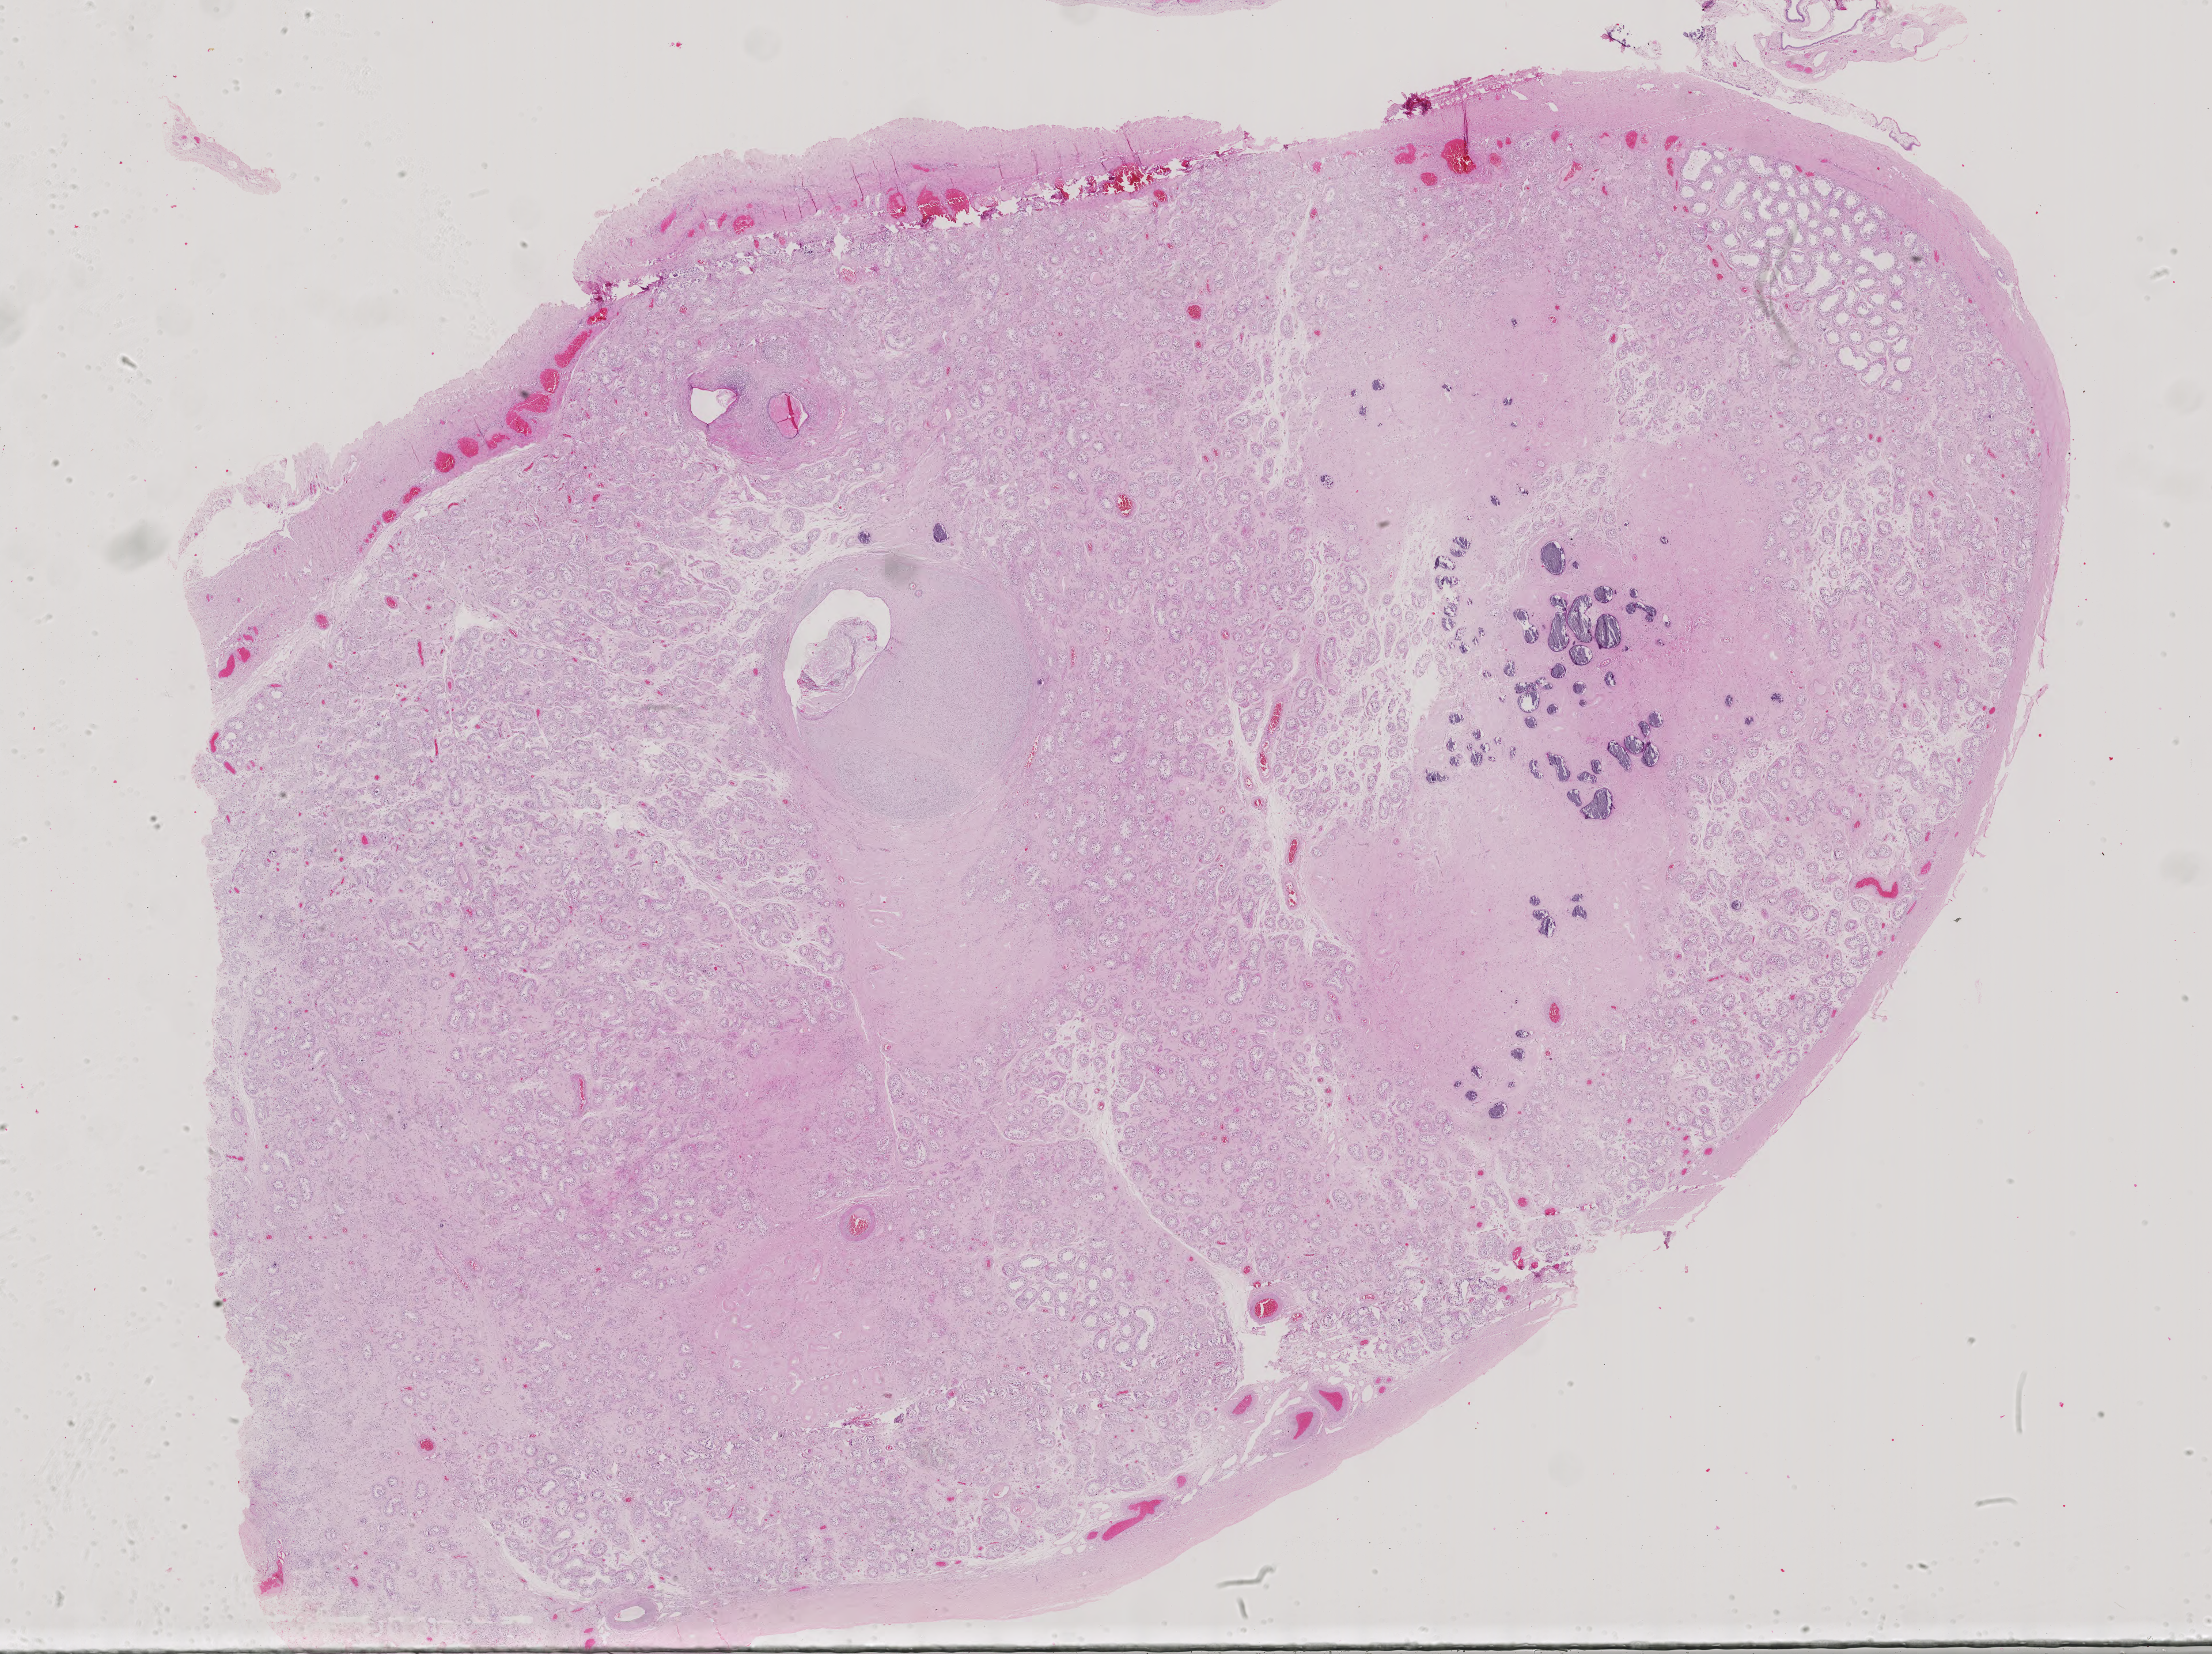
Hematoxylin and eosin (H&E) stained whole-slide image, shown as a low-resolution overview of the whole scanned area (about 28.0 x 20.9 mm), FFPE section, primary tumour sample from the testis. Male patient; age at initial diagnosis 27 years.
* pathologic diagnosis: Embryonal carcinoma, NOS
* AJCC pathologic stage: IIIA
* TNM: T2 N2 M1a
* laterality: left